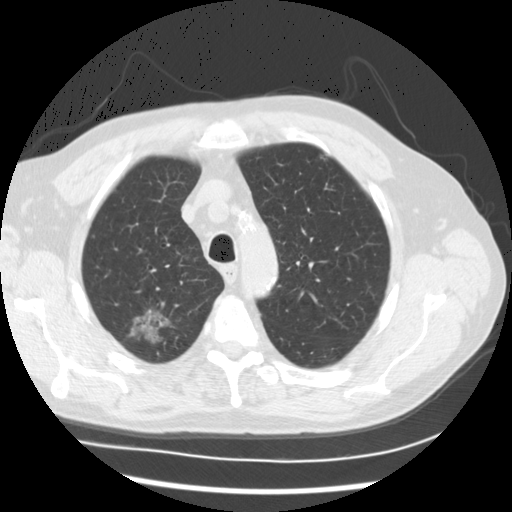
Low-dose screening chest CT, axial slice; baseline annual screen; lung window (W 1500 / L -600 HU); 2.5 mm slice thickness; 512 × 512 image matrix, field of view 360 × 360 mm. Male participant, aged 68 years at enrolment. Current smoker at enrolment.
Expert reader's lesion annotation, bounding box <114,291,188,362> (left, top, right, bottom; pixels). The screening reader recorded 3 non-calcified nodules or masses ≥4 mm on this exam (right upper lobe, right upper lobe, right lower lobe); which of them this box marks is not recorded. Official screen result: positive, change unspecified: nodule(s) >= 4 mm or enlarging nodule(s), mass(es), or other non-specific abnormalities suspicious for lung cancer. Lung cancer was diagnosed 90 days after this screen: adenocarcinoma, NOS, right upper lobe, right lower lobe, well differentiated (G1), stage IV (AJCC 6th edition), 35 mm at pathology.